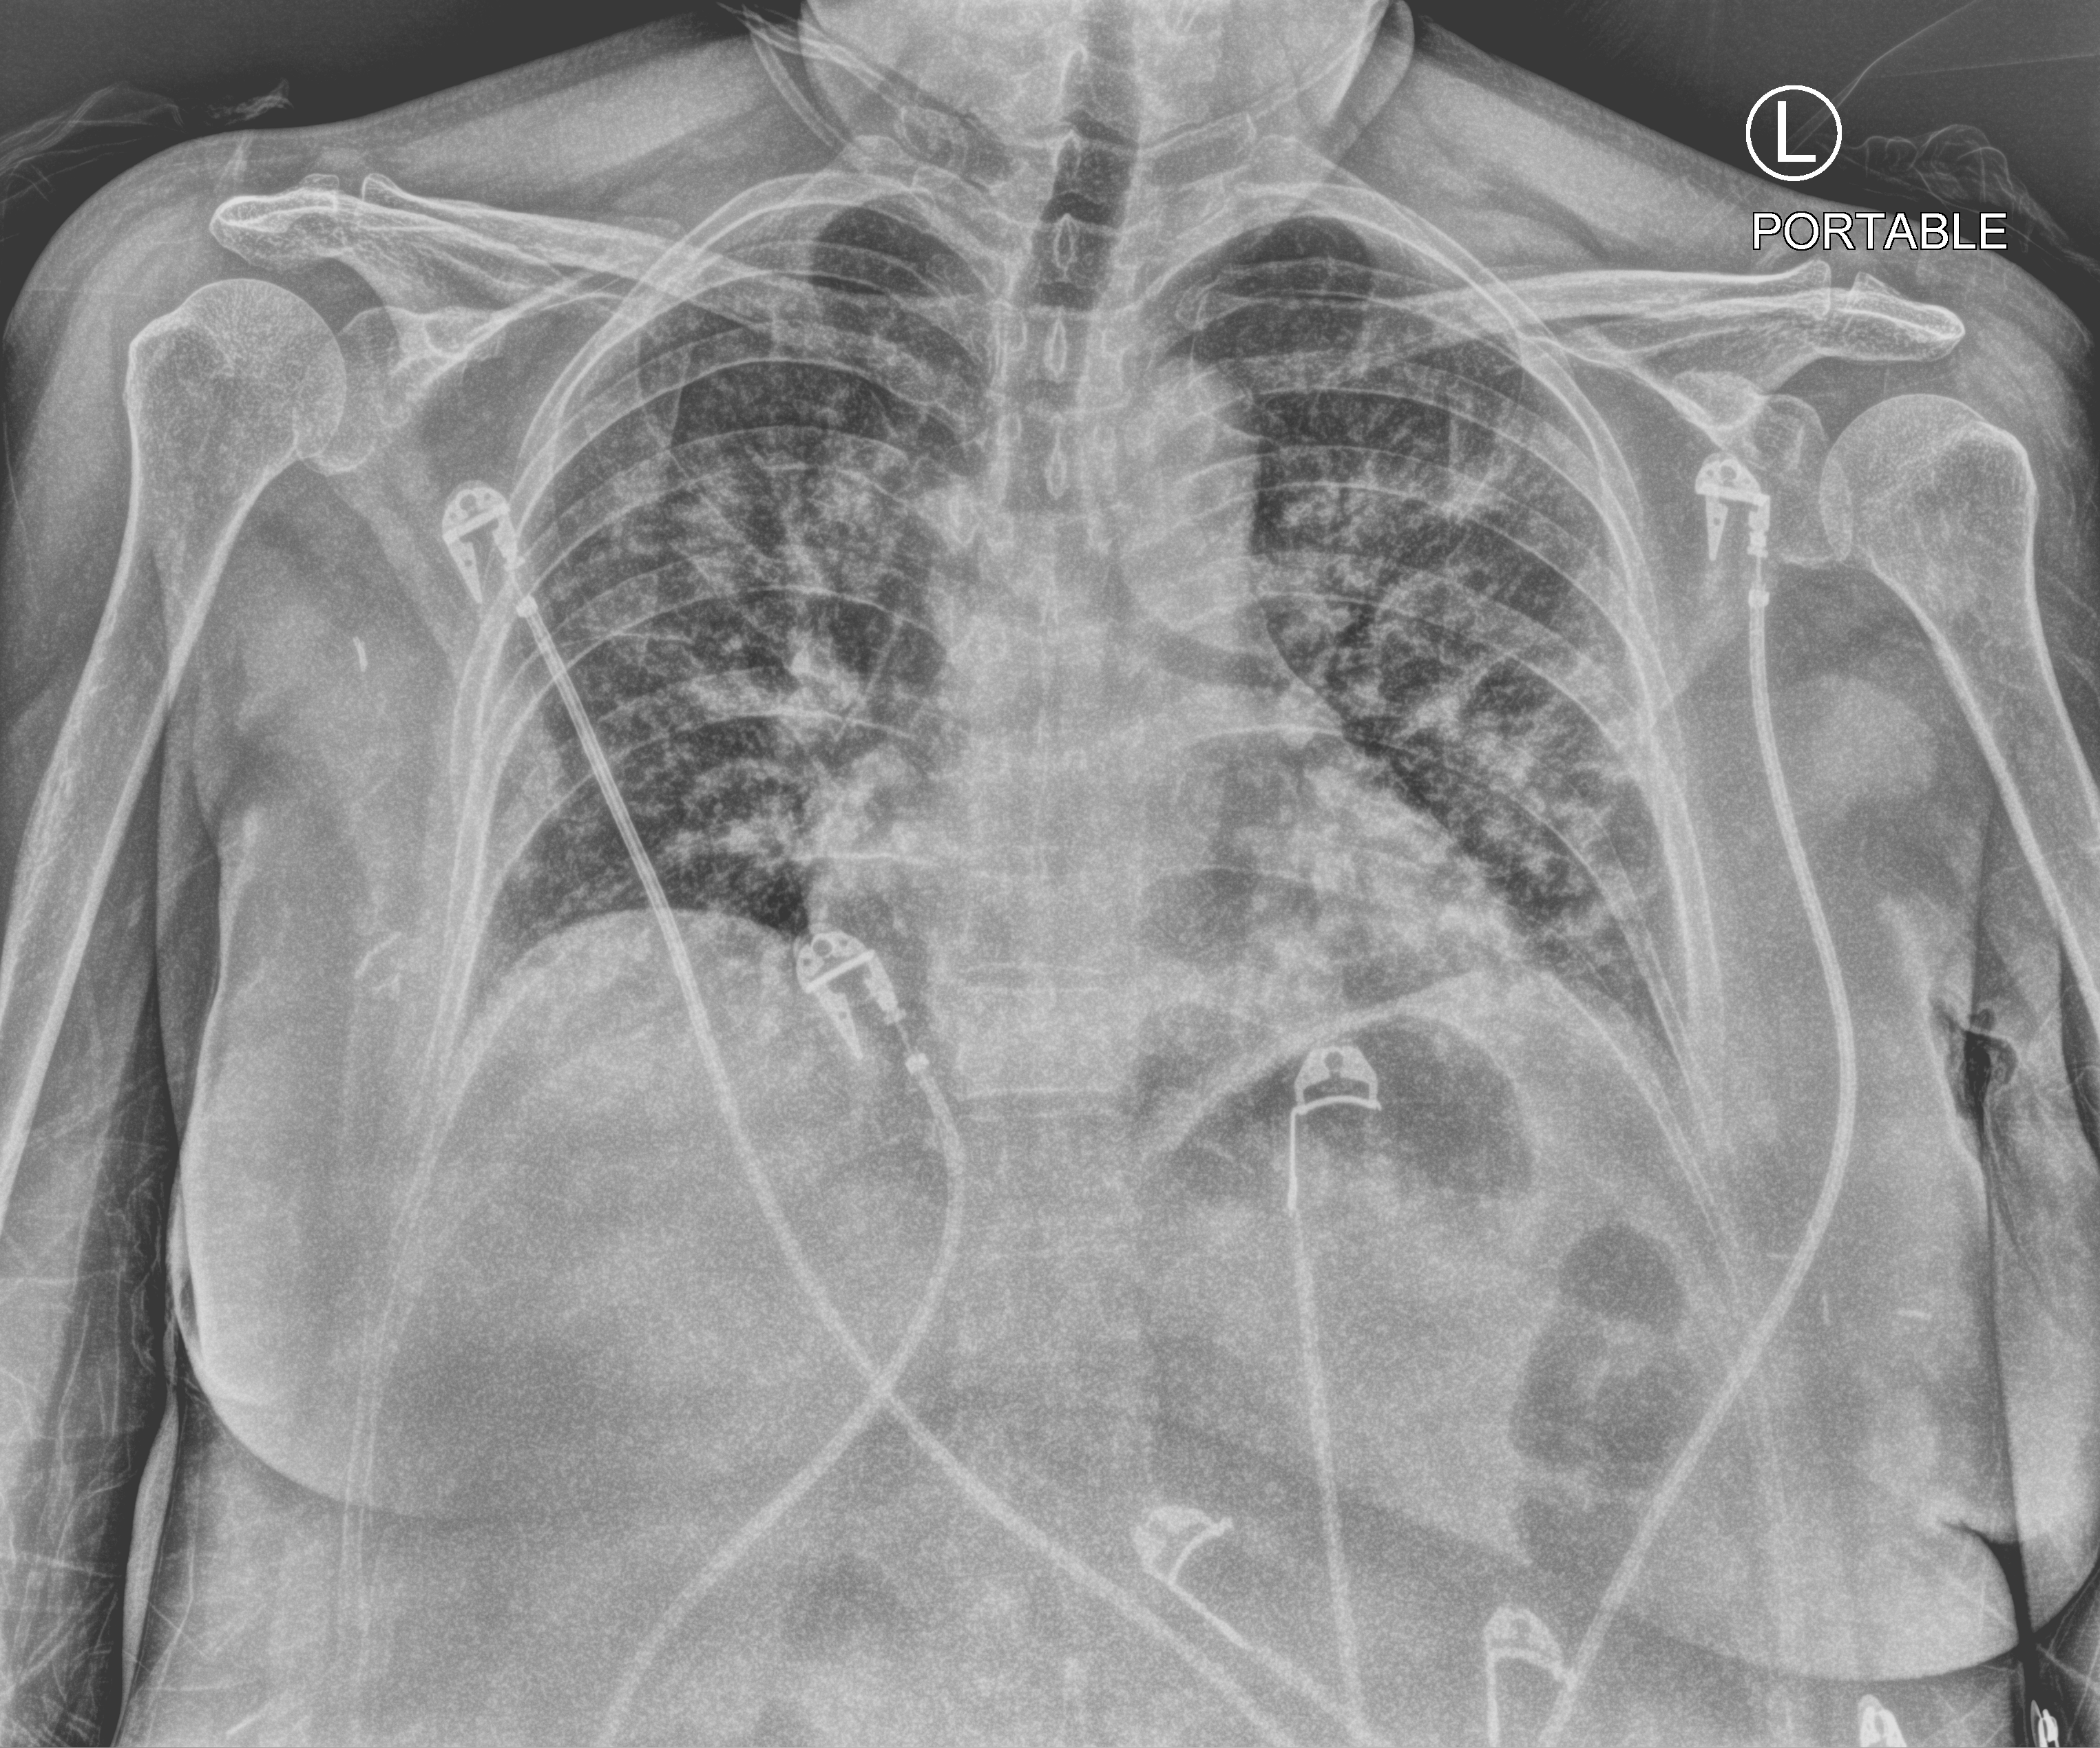
Bedside chest radiograph (computed radiography); anteroposterior (AP) projection. Female patient hospitalised with COVID-19, age 18–59 years.
Admission-level facts for this patient (not findings on this image; timing relative to this image not recorded): smoking status (admission record): never; mechanically ventilated during this hospital stay: yes.